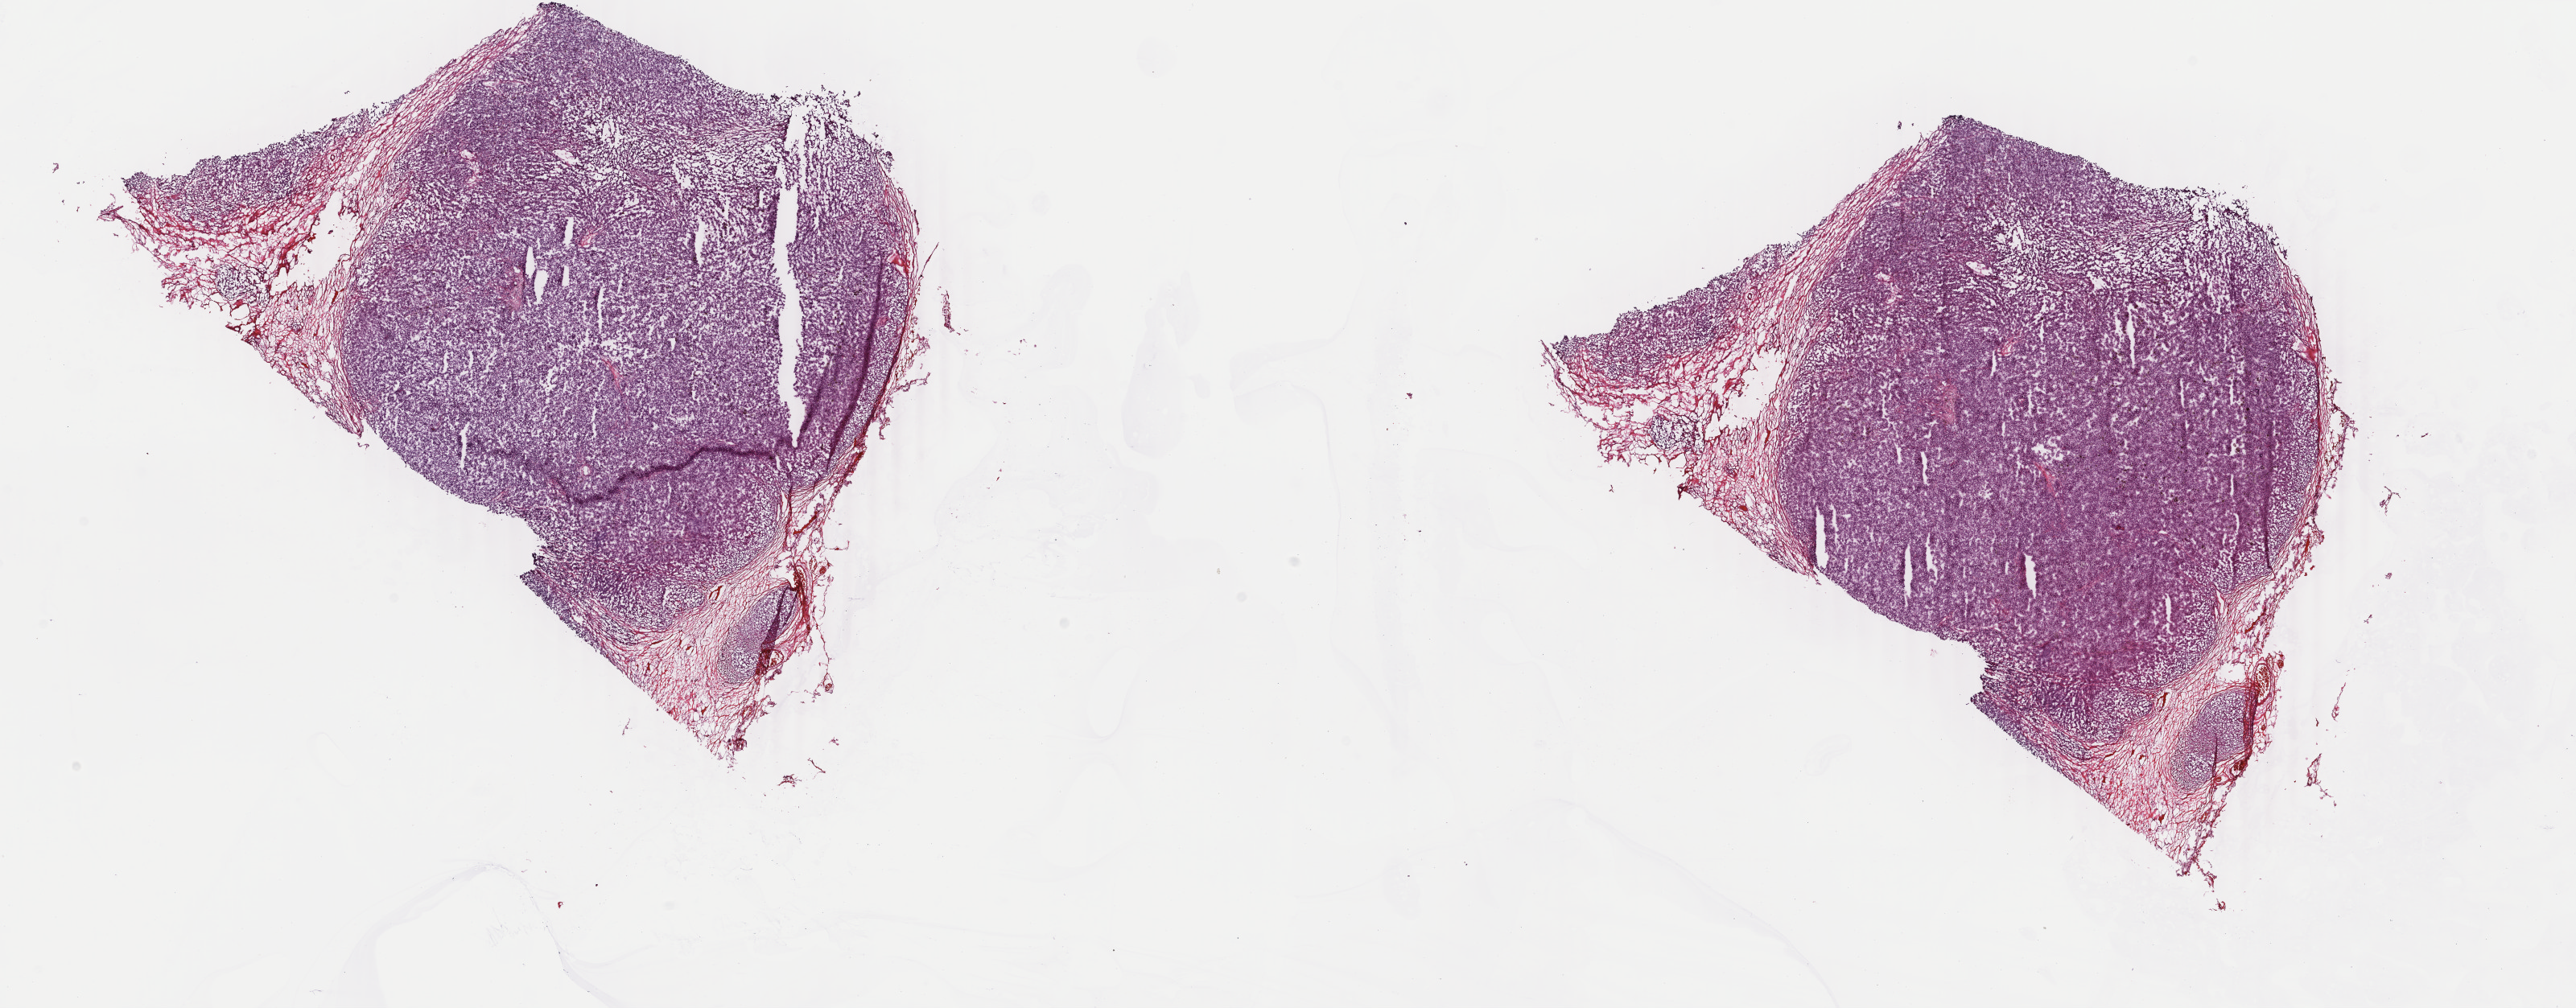
Whole-slide histology image, H&E-stained — low-resolution overview of the scanned area, about 25.5 x 10.0 mm (slide scanned at 40x). Frozen section. Metastatic tumour sample, sampled site: lymph node. Female, age 60 years at initial diagnosis. Composition of this section per pathologist review: tumour cells 100%, tumour nuclei 95%, normal cells 0%, stromal cells 0%, necrosis 0%. Infiltration values recorded for this section: lymphocyte infiltration 0%, monocyte infiltration 0%, neutrophil infiltration 0%.
- this section: metastatic tumour tissue
- patient diagnosis: Malignant melanoma, NOS